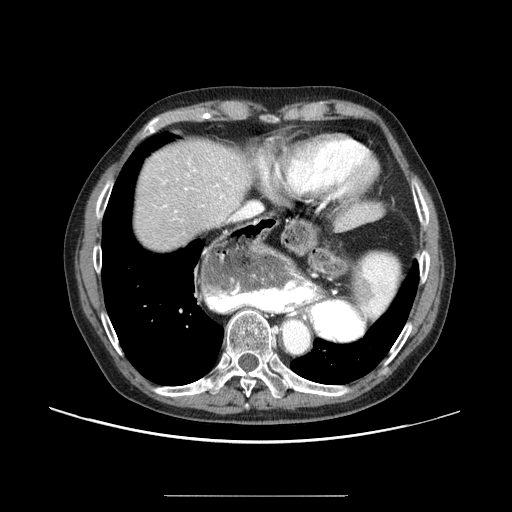
Contrast-enhanced abdominal CT (liver protocol), one axial slice. Slice 76 of 91 in the series (ordered by position). 100 kVp. One of 2 acquisitions stored at this slice position. Soft-tissue window (W 400 / L 40 HU). 512 × 512 image matrix, field of view 400 × 400 mm. From the clinical record (not read from this slice): diagnosis: hepatocellular carcinoma (patient treated with transarterial chemoembolisation; whether this scan precedes or follows treatment is not stated here); TNM stage (as recorded): Stage-I; Child-Pugh class: A; tumour differentiation: moderately differentiated.
Structures marked on this image (semi-automatic segmentation, software-assisted and operator-edited):
- abdominal aorta: bounding box <283,321,308,353> (left, top, right, bottom; pixels)
- liver parenchyma outside the tumour (the mass and vessels are separate outlines, so this box may not span the whole liver): <134,140,252,250>
- liver vessels: <185,177,228,198>